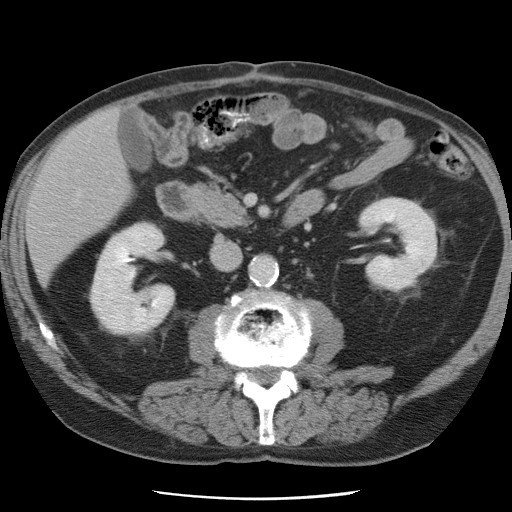
Contrast-enhanced abdominal CT, one axial slice. Slice 25 of 78 in the series (ordered by position). Intravenous contrast given. Soft-tissue window (W 400 / L 40 HU). 5 mm slice thickness. 512 × 512 image matrix. Male patient, age 75 years. From the clinical record (not read from this slice): diagnosis: colorectal cancer liver metastases, imaged before liver resection.
Outlined on this slice (outlined manually by an expert reader):
- liver: bounding box <28,110,133,281> (left, top, right, bottom; pixels)
- planned liver remnant (the part of the liver to remain after resection): <28,119,132,281>